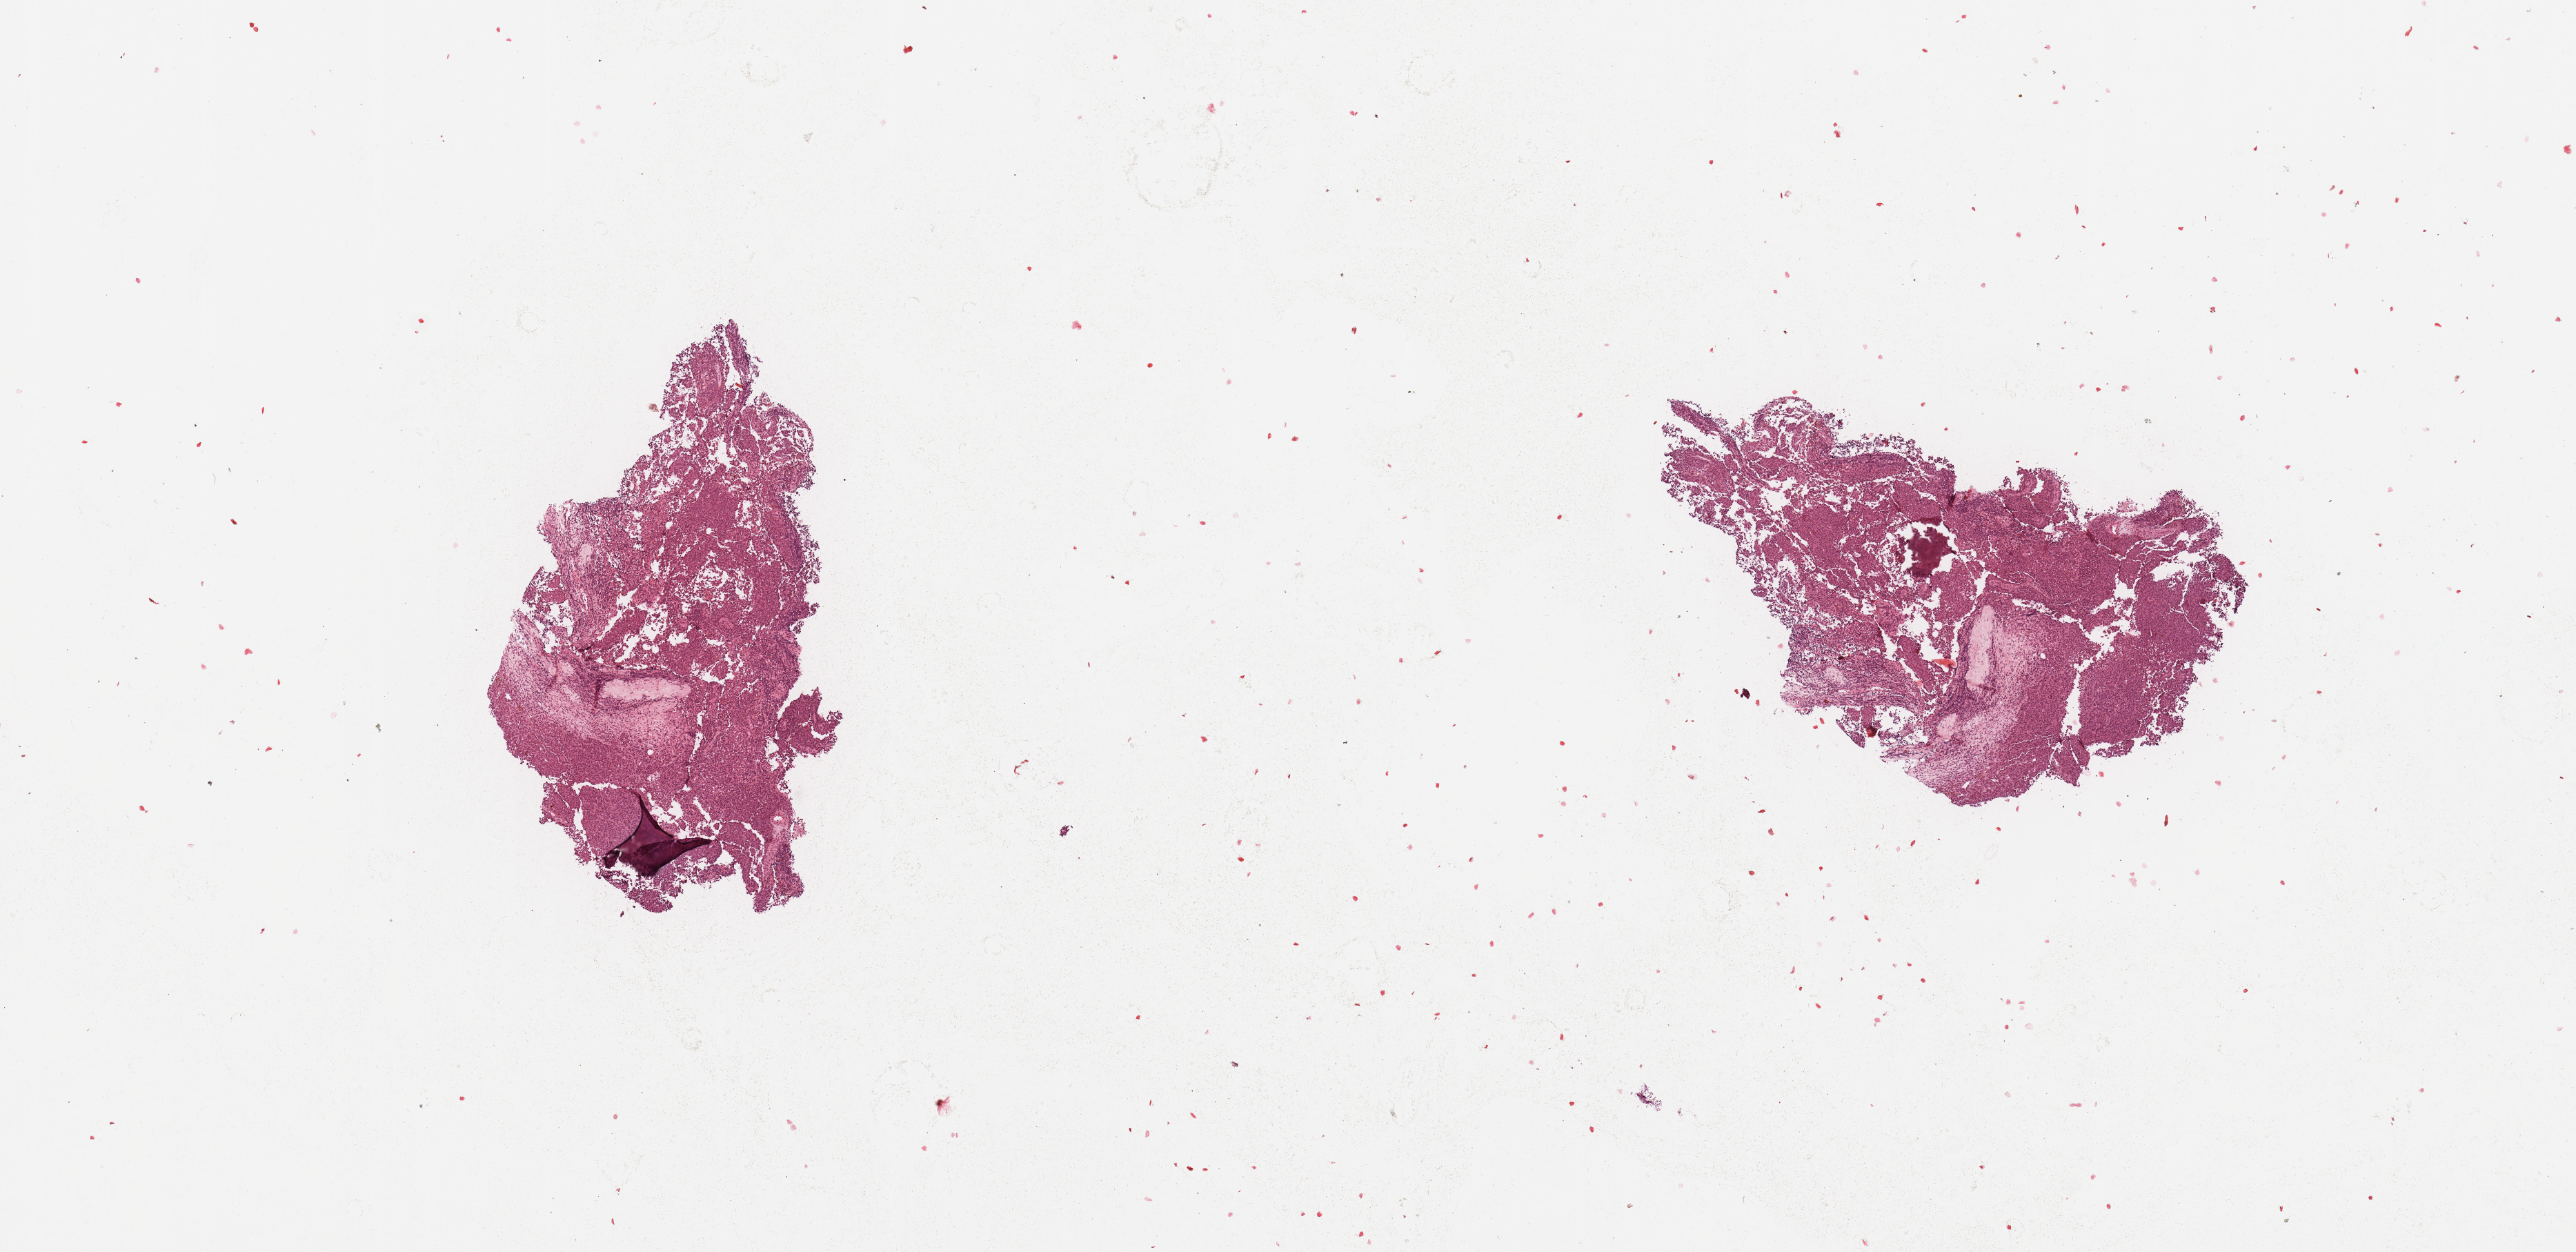
Digitized H&E-stained tissue section (whole slide), low-resolution overview of the scanned area, about 14.8 x 7.2 mm; tumour tissue sample, sampled site: lymph node. 76-year-old male patient. Composition of this section per pathologist review: tumour nuclei 90%, necrosis 10%.
This section: metastatic tumour tissue. Patient diagnosis: Malignant melanoma, NOS.